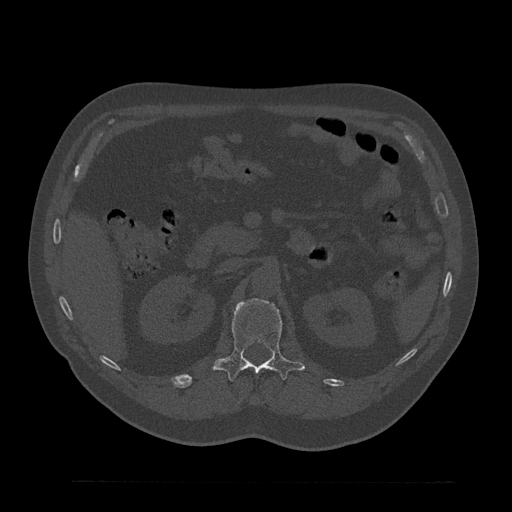
CT including the spine, one axial slice; slice 171 of 797 in the series (ordered by position); reconstruction kernel Br40s/3; 120 kVp; bone window (W 1800 / L 400 HU); 0.5 mm slice thickness; 512 × 512 image matrix, field of view 430 × 430 mm. Patient: male, 61 years. From the clinical record (not read from this slice): primary cancer: prostate.
Outlined on this slice (semi-automatically segmented with operator editing):
- L1 vertebra: box from (x=213, y=299) to (x=305, y=382) px